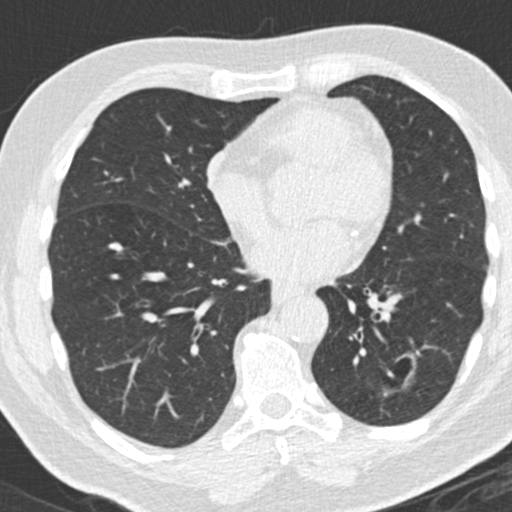
Low-dose screening chest CT, axial slice; third screening round (two years after baseline); lung window (W 1500 / L -600 HU); 2 mm slice thickness; 120 kVp; slice 98 of 180 in the series; 512 × 512 image matrix, field of view 300 × 300 mm. Male, age 66 years at enrolment.
- Lesion marked by an expert reader, bounding box [x1, y1, x2, y2] px = [355, 343, 427, 428].
- Screening reader's record for this exam (one nodule recorded; not confirmed to be the boxed lesion): non-calcified nodule or mass ≥4 mm, left lower lobe, 31 × 24 mm, spiculated (stellate) margins, pre-existing on the prior screen: yes; interval growth: yes.
- Official screen result: positive, other.
- Later outcome: lung cancer diagnosed 56 days after this screen — adenocarcinoma, NOS, left lower lobe, poorly differentiated (G3), stage IB (AJCC 6th edition), 38 mm at pathology.